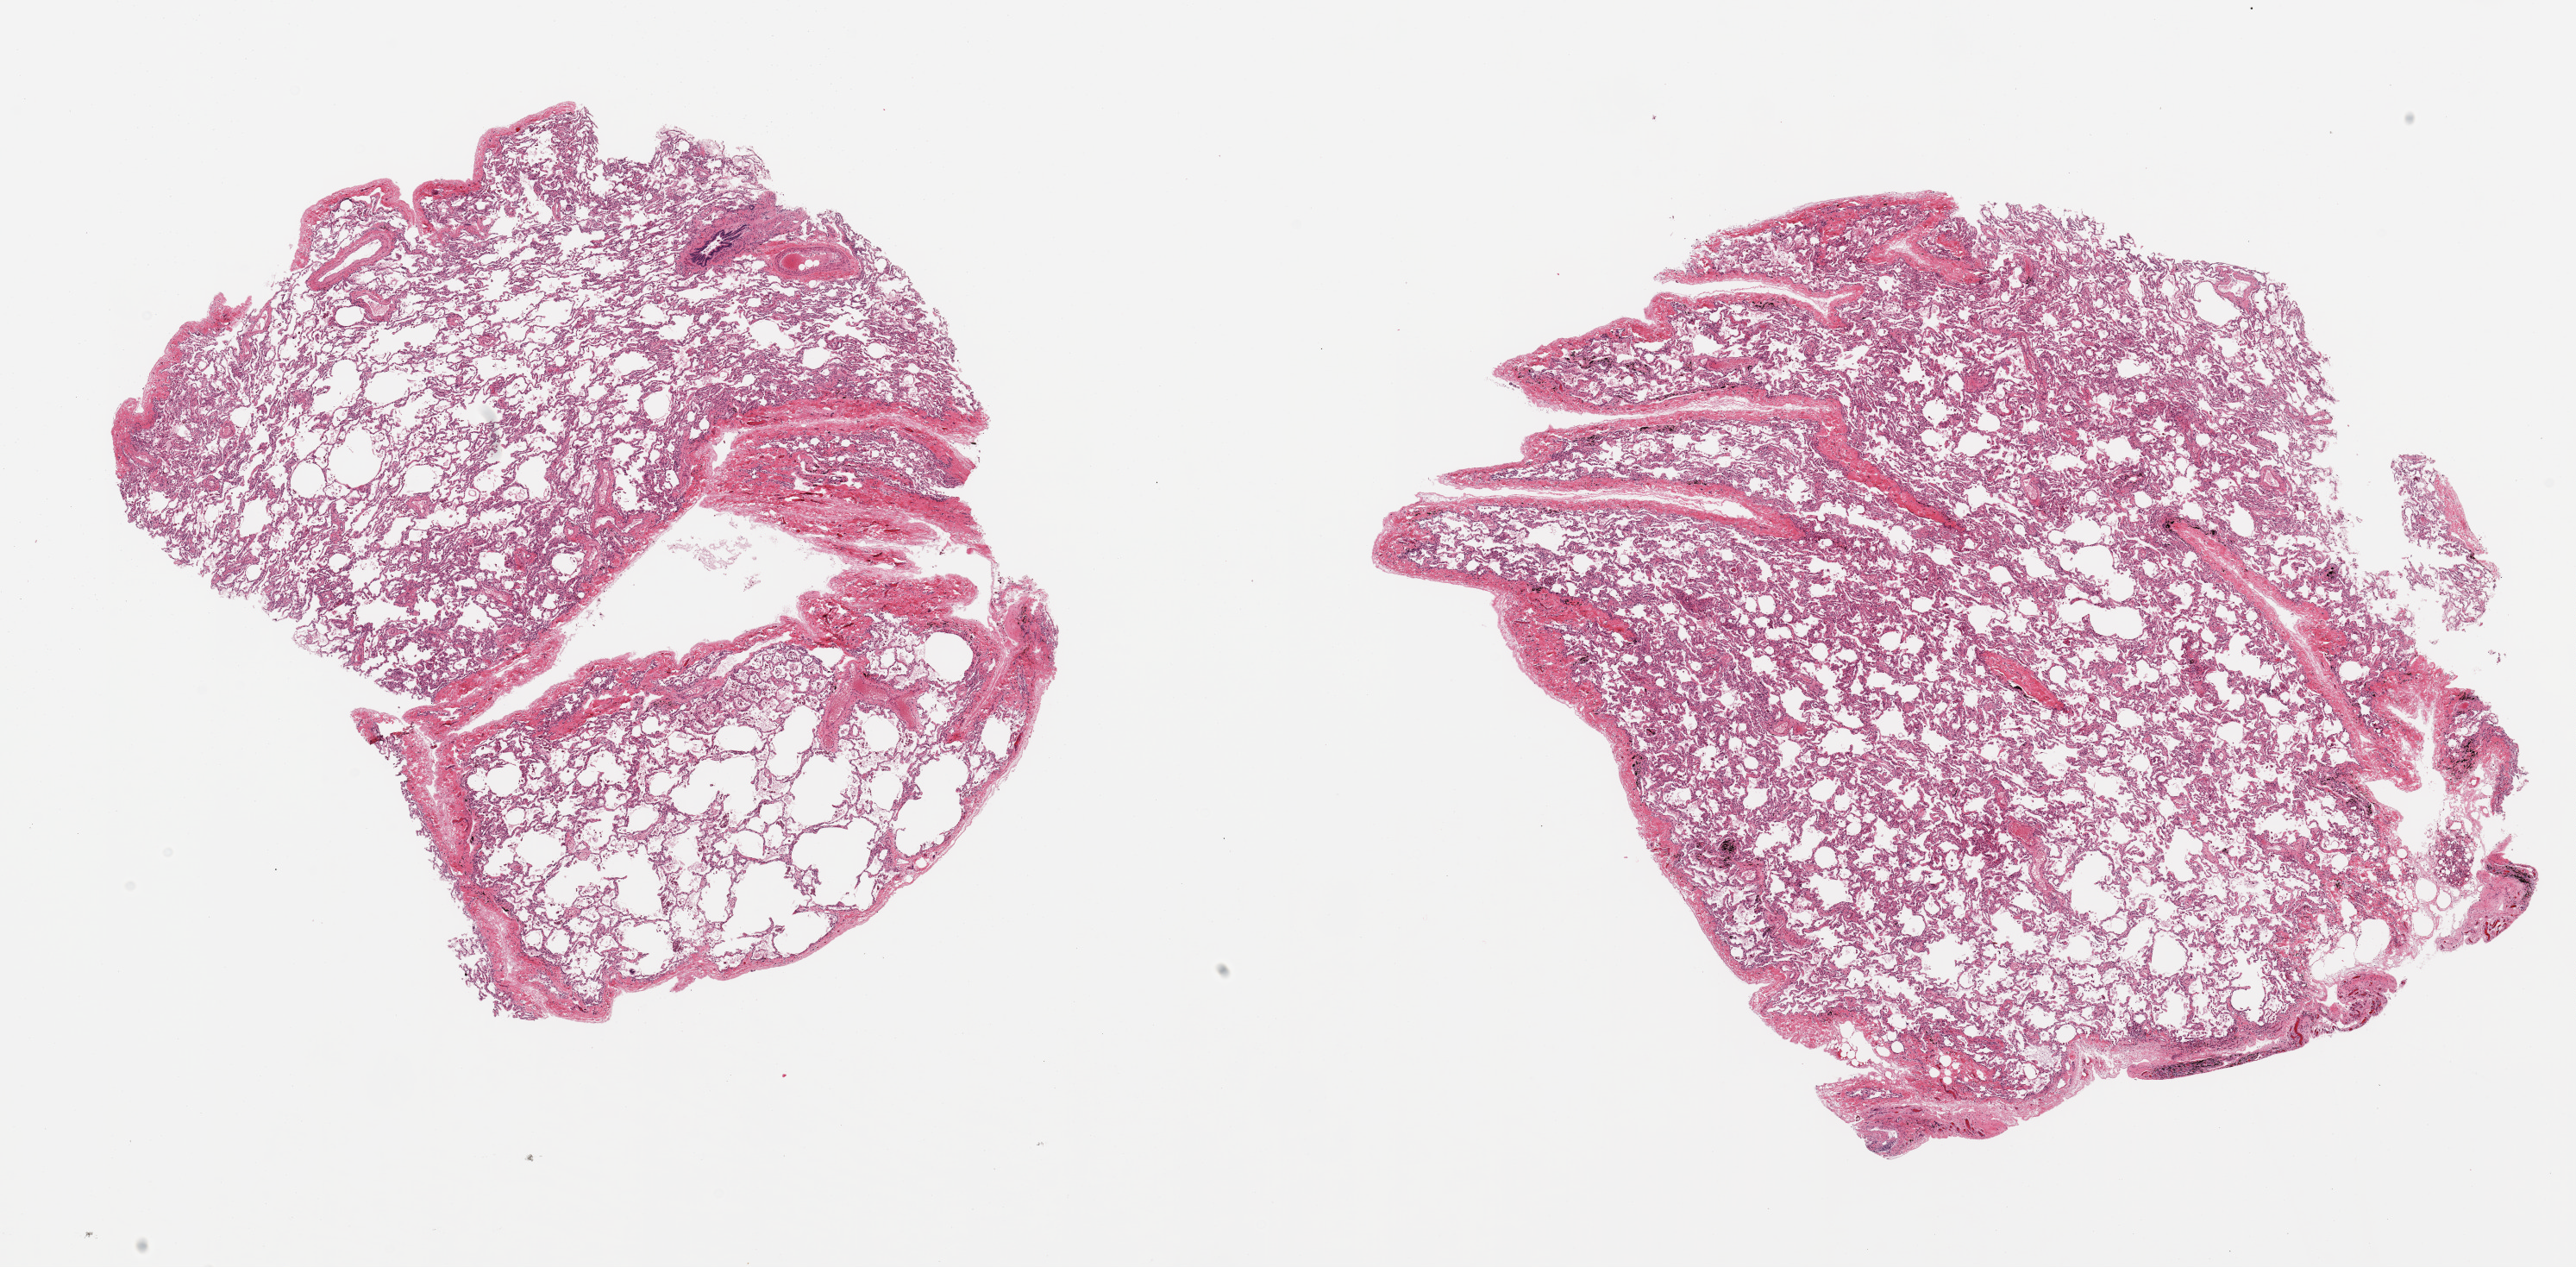
Whole-slide image, H&E stain — a low-resolution overview of the entire scanned area, about 23.6 x 11.6 mm, PAXgene-fixed, paraffin-embedded tissue, section of lung (target tissue), tissue donor sample.
* review note (as recorded): 2 pieces; covered by pleura, some anthracotic-like pigment